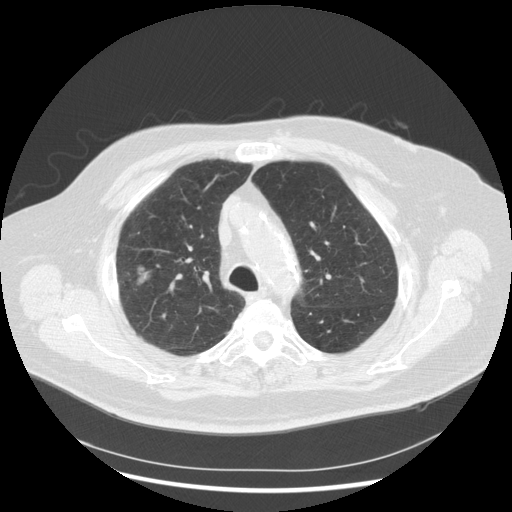
Low-dose screening chest CT, one axial slice. Position 207 of 263 along the scan axis. Lung window (W 1500 / L -600 HU). 512 × 512 image matrix.
Annotated regions visible in this slice (expert manual segmentation):
- lesion 1 (tumor, upper lobe of right lung): bounding box (x1, y1, x2, y2) in pixels: (137, 266, 151, 285)